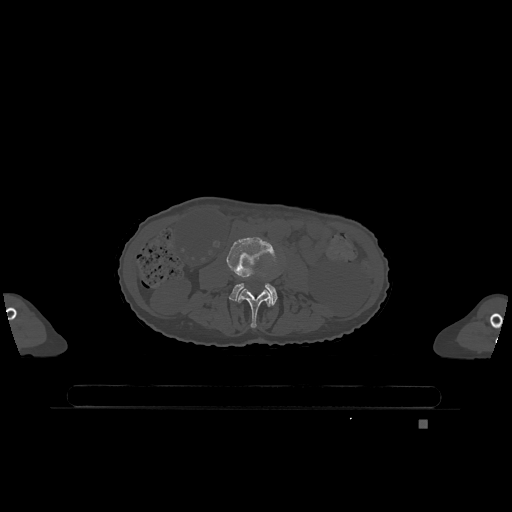
CT including the spine, one axial slice. Position 332 of 1317 along the scan axis. Bone window (W 1800 / L 400 HU). 0.5 mm slice thickness. 512 × 512 image matrix, field of view 500 × 500 mm. Female patient, age 74 years. From the clinical record (not read from this slice): primary cancer: lung; vertebrae with lytic lesions (as recorded): T1, T4, T5, T6, L4, L5.
Structures marked on this image (semi-automatically segmented with operator editing):
- L3 vertebra: bounding box (x1, y1, x2, y2) in pixels: (238, 289, 272, 328)
- L4 vertebra: (227, 237, 278, 305)